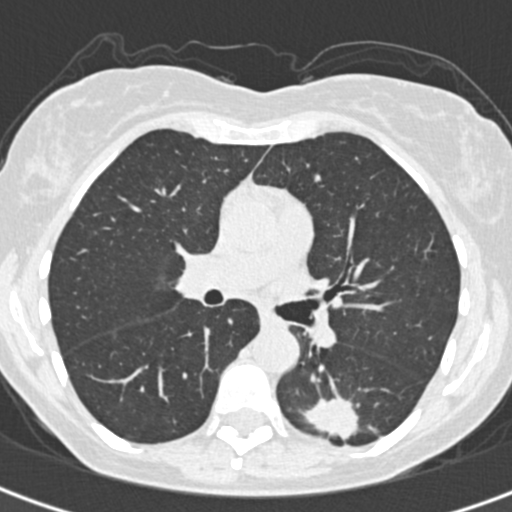
Low-dose screening chest CT, one axial slice. Position 197 of 328 along the scan axis. 120 kVp. Lung window (W 1500 / L -600 HU). 1 mm slice thickness. 512 × 512 image matrix.
Annotated regions visible in this slice (outlined manually by an expert reader):
- lesion 1 (tumor, lower lobe of left lung): bounding box [x1, y1, x2, y2] px = [303, 397, 358, 439]